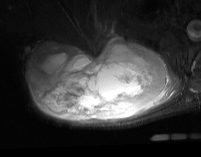
MRI of an extremity soft-tissue mass, one axial slice; STIR; MR volume resampled by the dataset authors to the PET/CT grid (not the native acquisition matrix); 201 × 157 image matrix. Male patient. Case-level facts recorded for this patient, not image findings: histological type: pleiomorphic spindle cell undifferentiated; grade: high; site of the primary tumour: right parascapusular.
Outlined on this slice (expert contour drawn on MRI and transferred to this co-registered scan by the dataset authors):
- gross tumour volume including surrounding oedema: box from (x=28, y=36) to (x=182, y=124) px
- gross tumour volume (mass): (x=28, y=39)–(x=168, y=120)